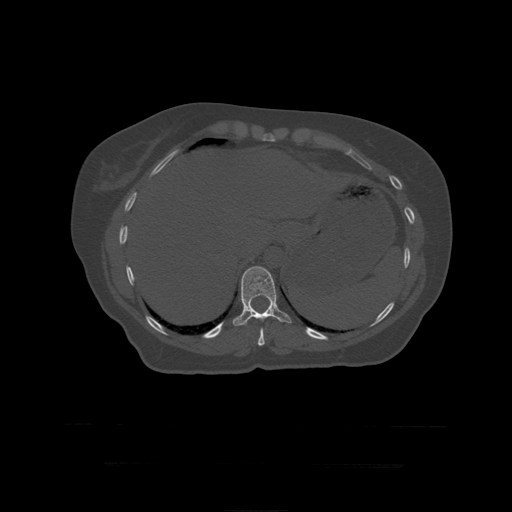
CT including the spine, one axial slice. Slice 224 of 399 in the series (ordered by position). Bone window (W 1800 / L 400 HU). 1.25 mm slice thickness. 512 × 512 image matrix, field of view 450 × 450 mm. Patient age 41 years. From the clinical record (not read from this slice): primary cancer: breast.
Annotated regions visible in this slice (semi-automatic segmentation, software-assisted and operator-edited):
- T10 vertebra: bounding box <258,328,265,346> (left, top, right, bottom; pixels)
- T11 vertebra: <232,266,292,326>